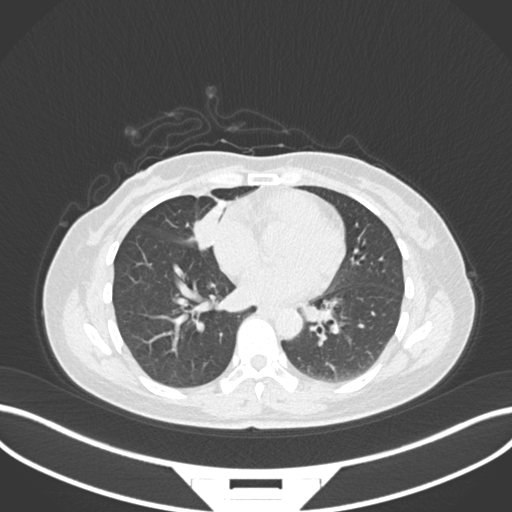
Chest CT, one axial slice; 120 kVp; lung window (W 1500 / L -600 HU); 1 mm slice thickness; 512 × 512 image matrix, field of view 400 × 400 mm. Female patient, age 43 years. Case-level facts recorded for this patient, not image findings: clinical TNM (as recorded): T1c N3 M1; histopathological grade: G1.
Outlined on this slice (rectangle marked by the reading radiologist):
- lung tumour (recorded histology: adenocarcinoma): bounding box [x1, y1, x2, y2] px = [187, 201, 226, 257]